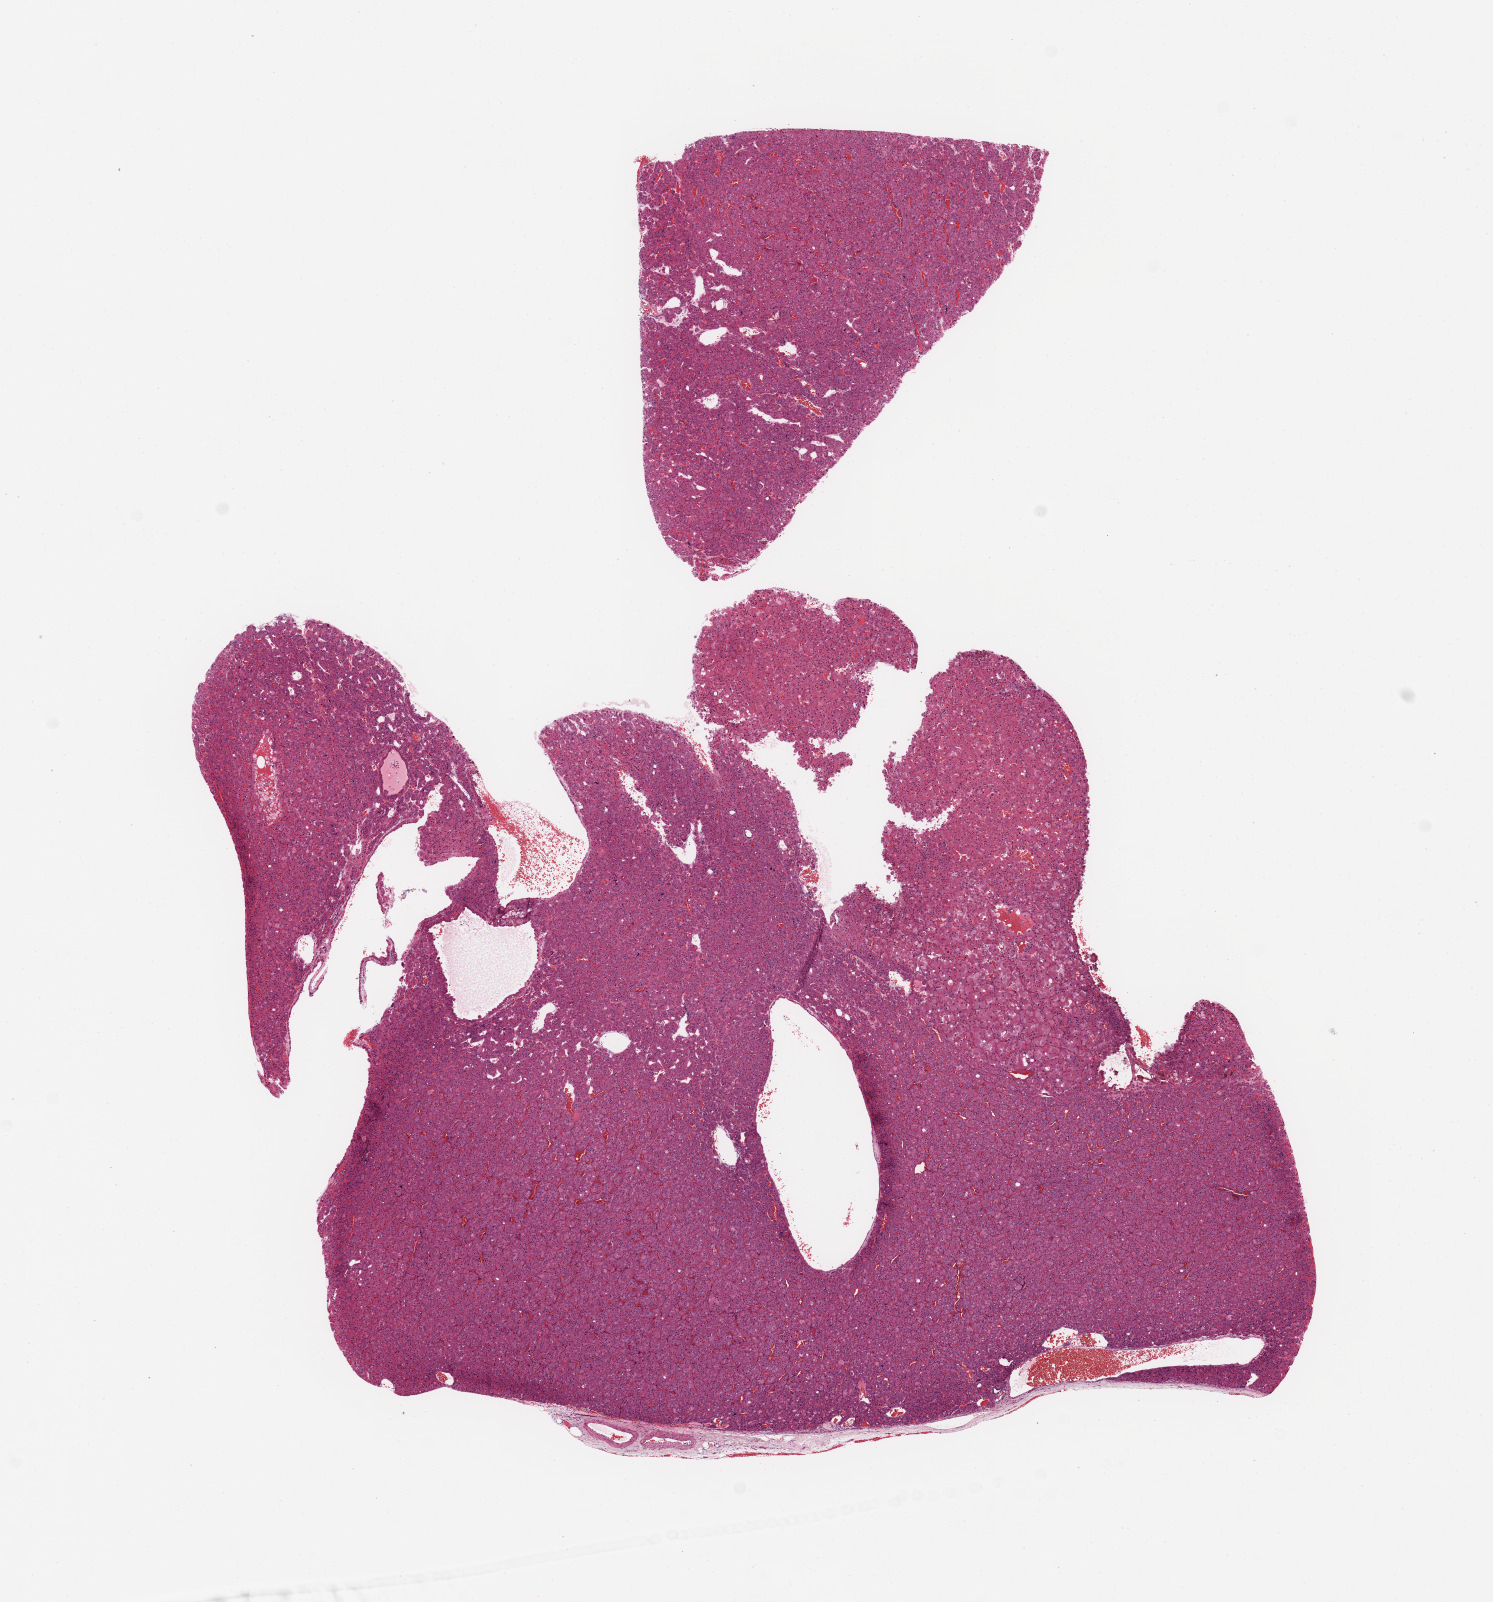
Whole-slide histology image, H&E-stained, a low-resolution overview of the entire scanned area, about 11.8 x 12.7 mm. Kidney, tumour tissue. Female, 73 y/o. Histologic grade: G1 (well differentiated).
Diagnosis: Renal cell carcinoma, NOS. AJCC pathologic stage: I.